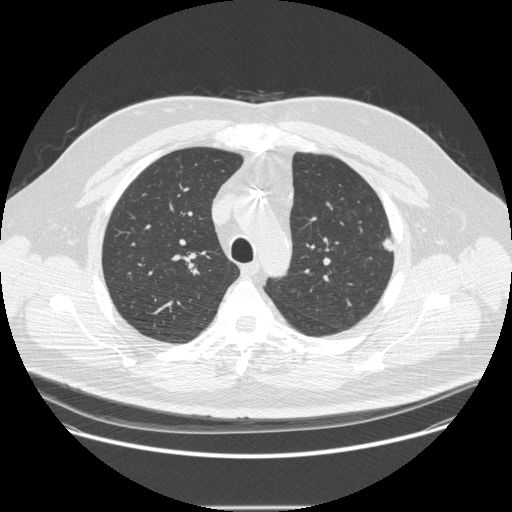
Axial slice from a low-dose chest CT screening exam; second annual screen; lung window (W 1500 / L -600 HU); standard (soft-tissue) reconstruction kernel (STANDARD); 120 kVp; slice 73 of 251 in the series; 512 × 512 image matrix, field of view 410 × 410 mm. Male participant, aged 55 years at enrolment.
Expert reader's lesion annotation, box from (x=373, y=229) to (x=405, y=251) px. The screening reader recorded 2 non-calcified nodules or masses ≥4 mm on this exam (left upper lobe, left upper lobe); which of them this box marks is not recorded. Official screen result: positive, other. Participant outcome: lung cancer diagnosed 60 days after this screen — adenocarcinoma, NOS, left upper lobe, moderately differentiated (G2), stage IA (AJCC 6th edition), 9 mm at pathology.